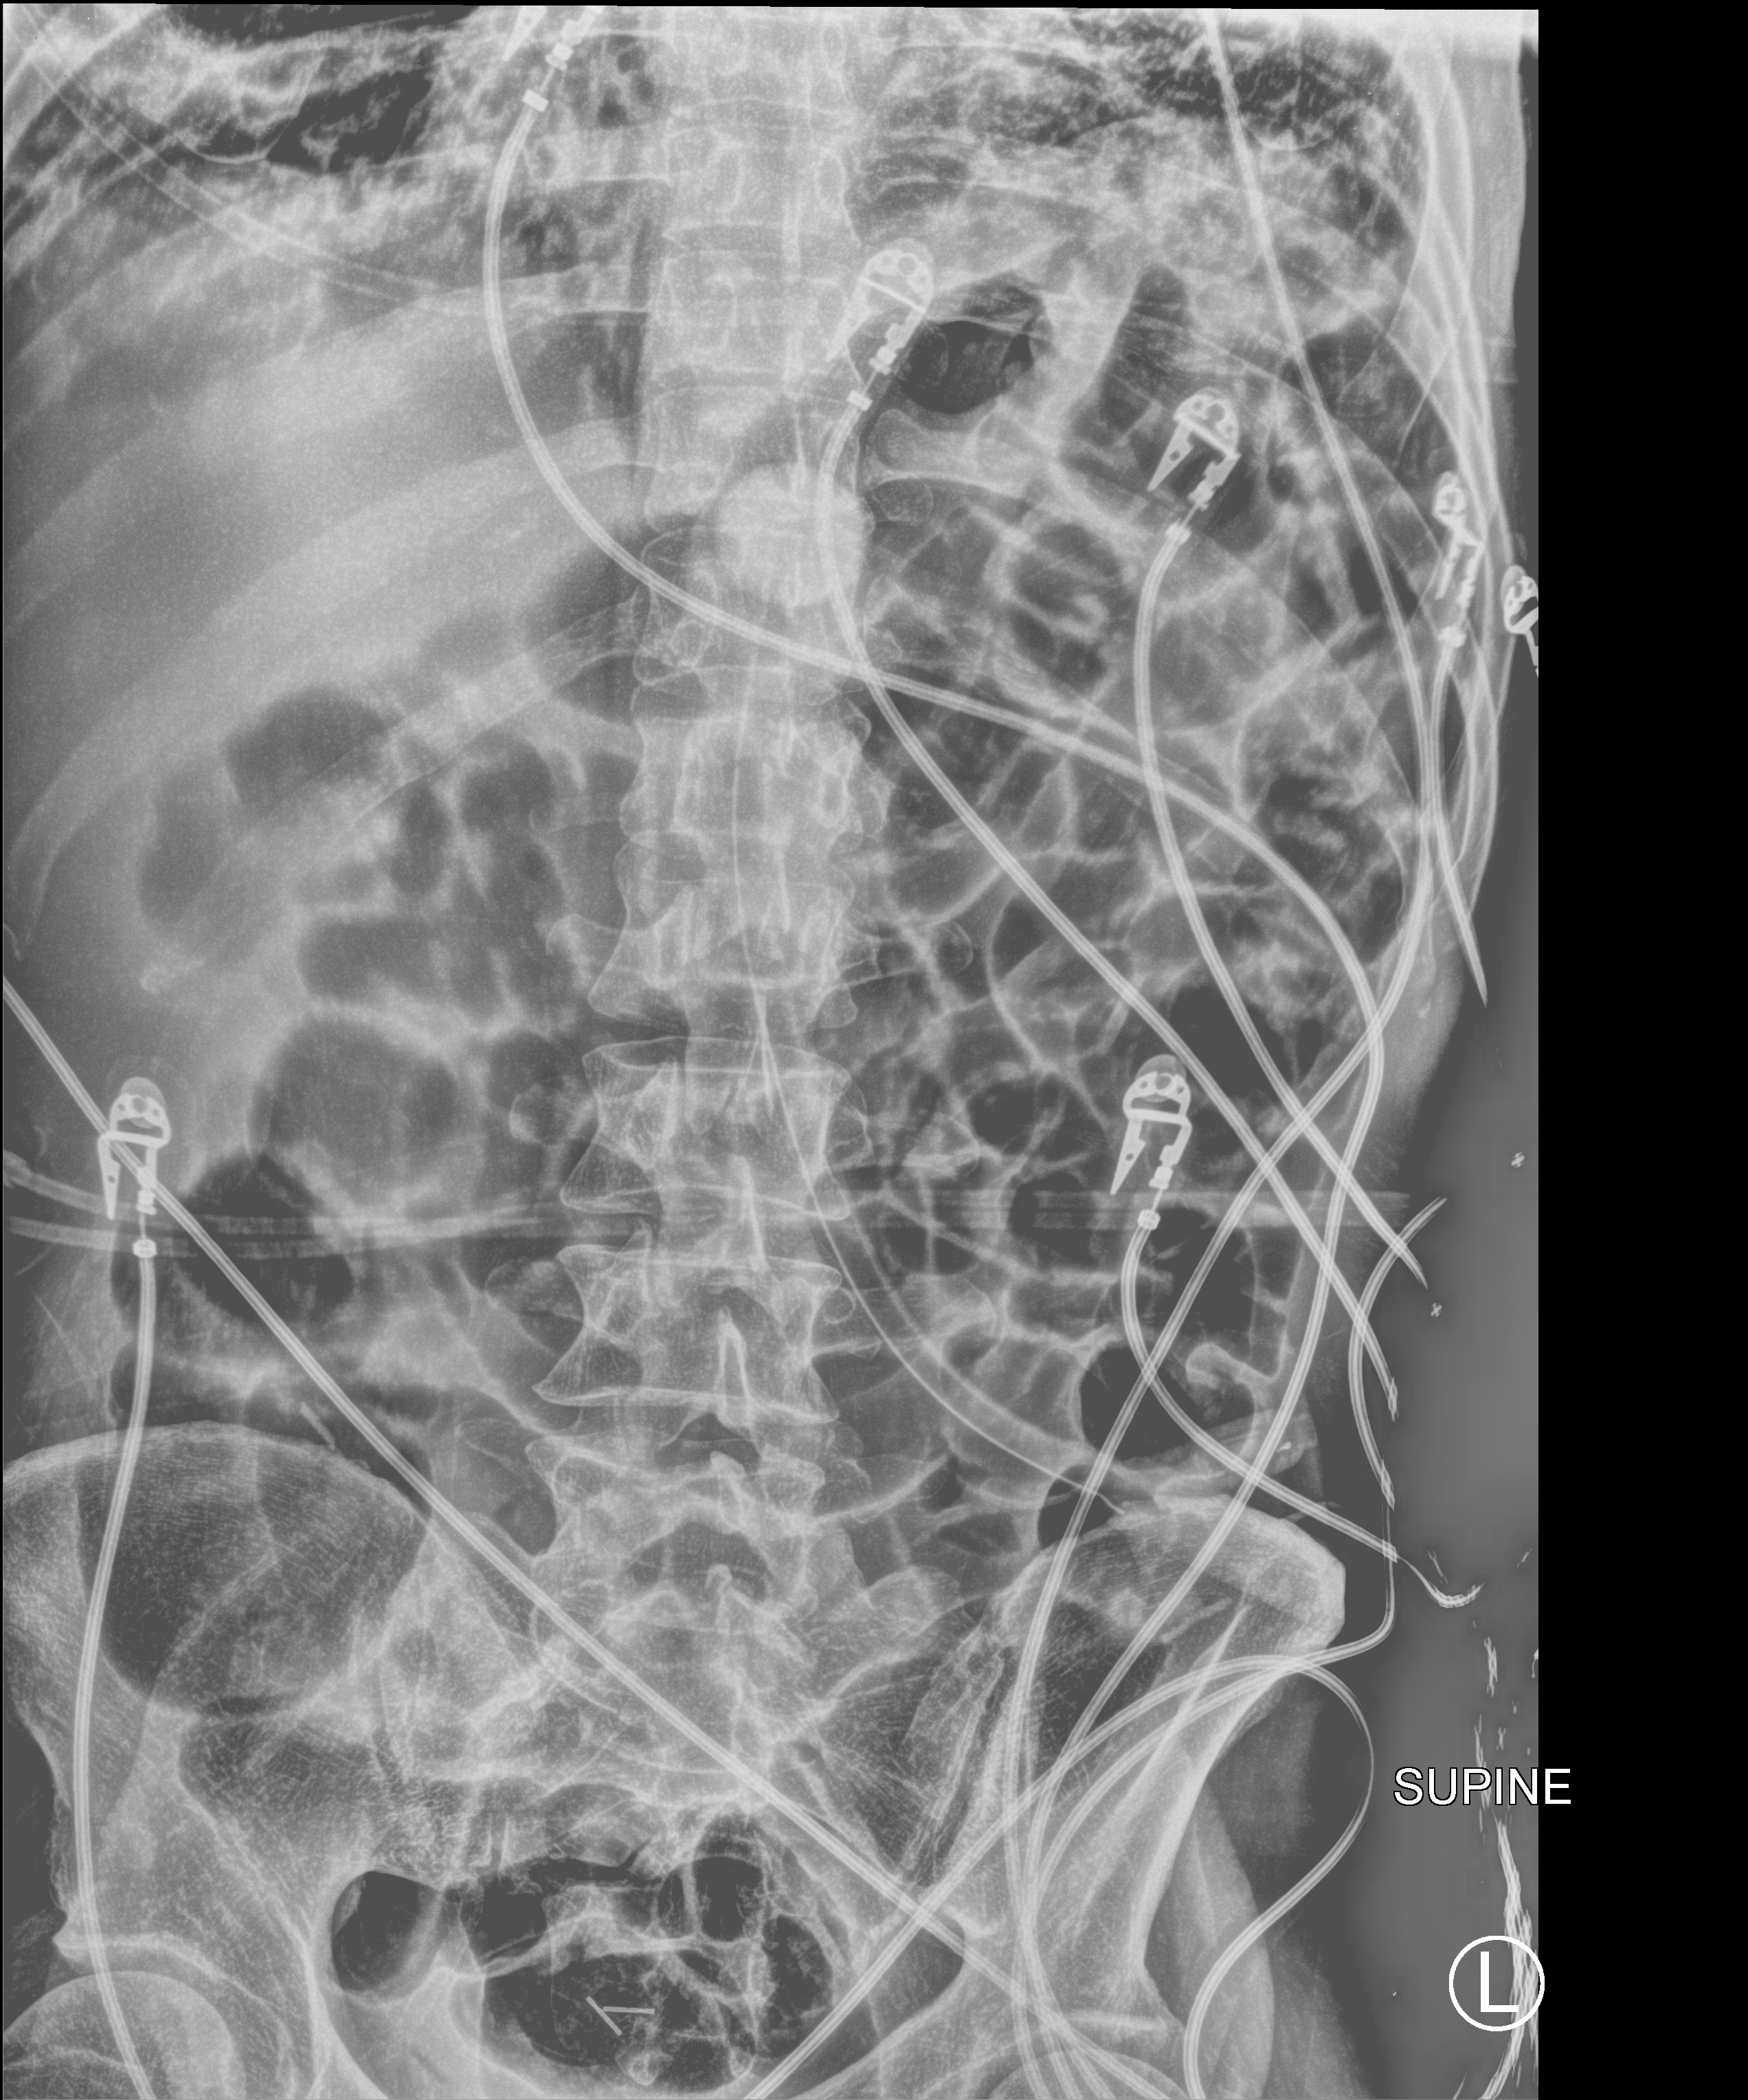
Portable abdomen radiograph, anteroposterior (AP) projection. Patient hospitalised with COVID-19; male, aged 18–59 years.
Admission-level facts for this patient (not findings on this image; timing relative to this image not recorded):
- diabetes (admission record): yes
- other chronic lung disease (admission record): no
- smoking status (admission record): never